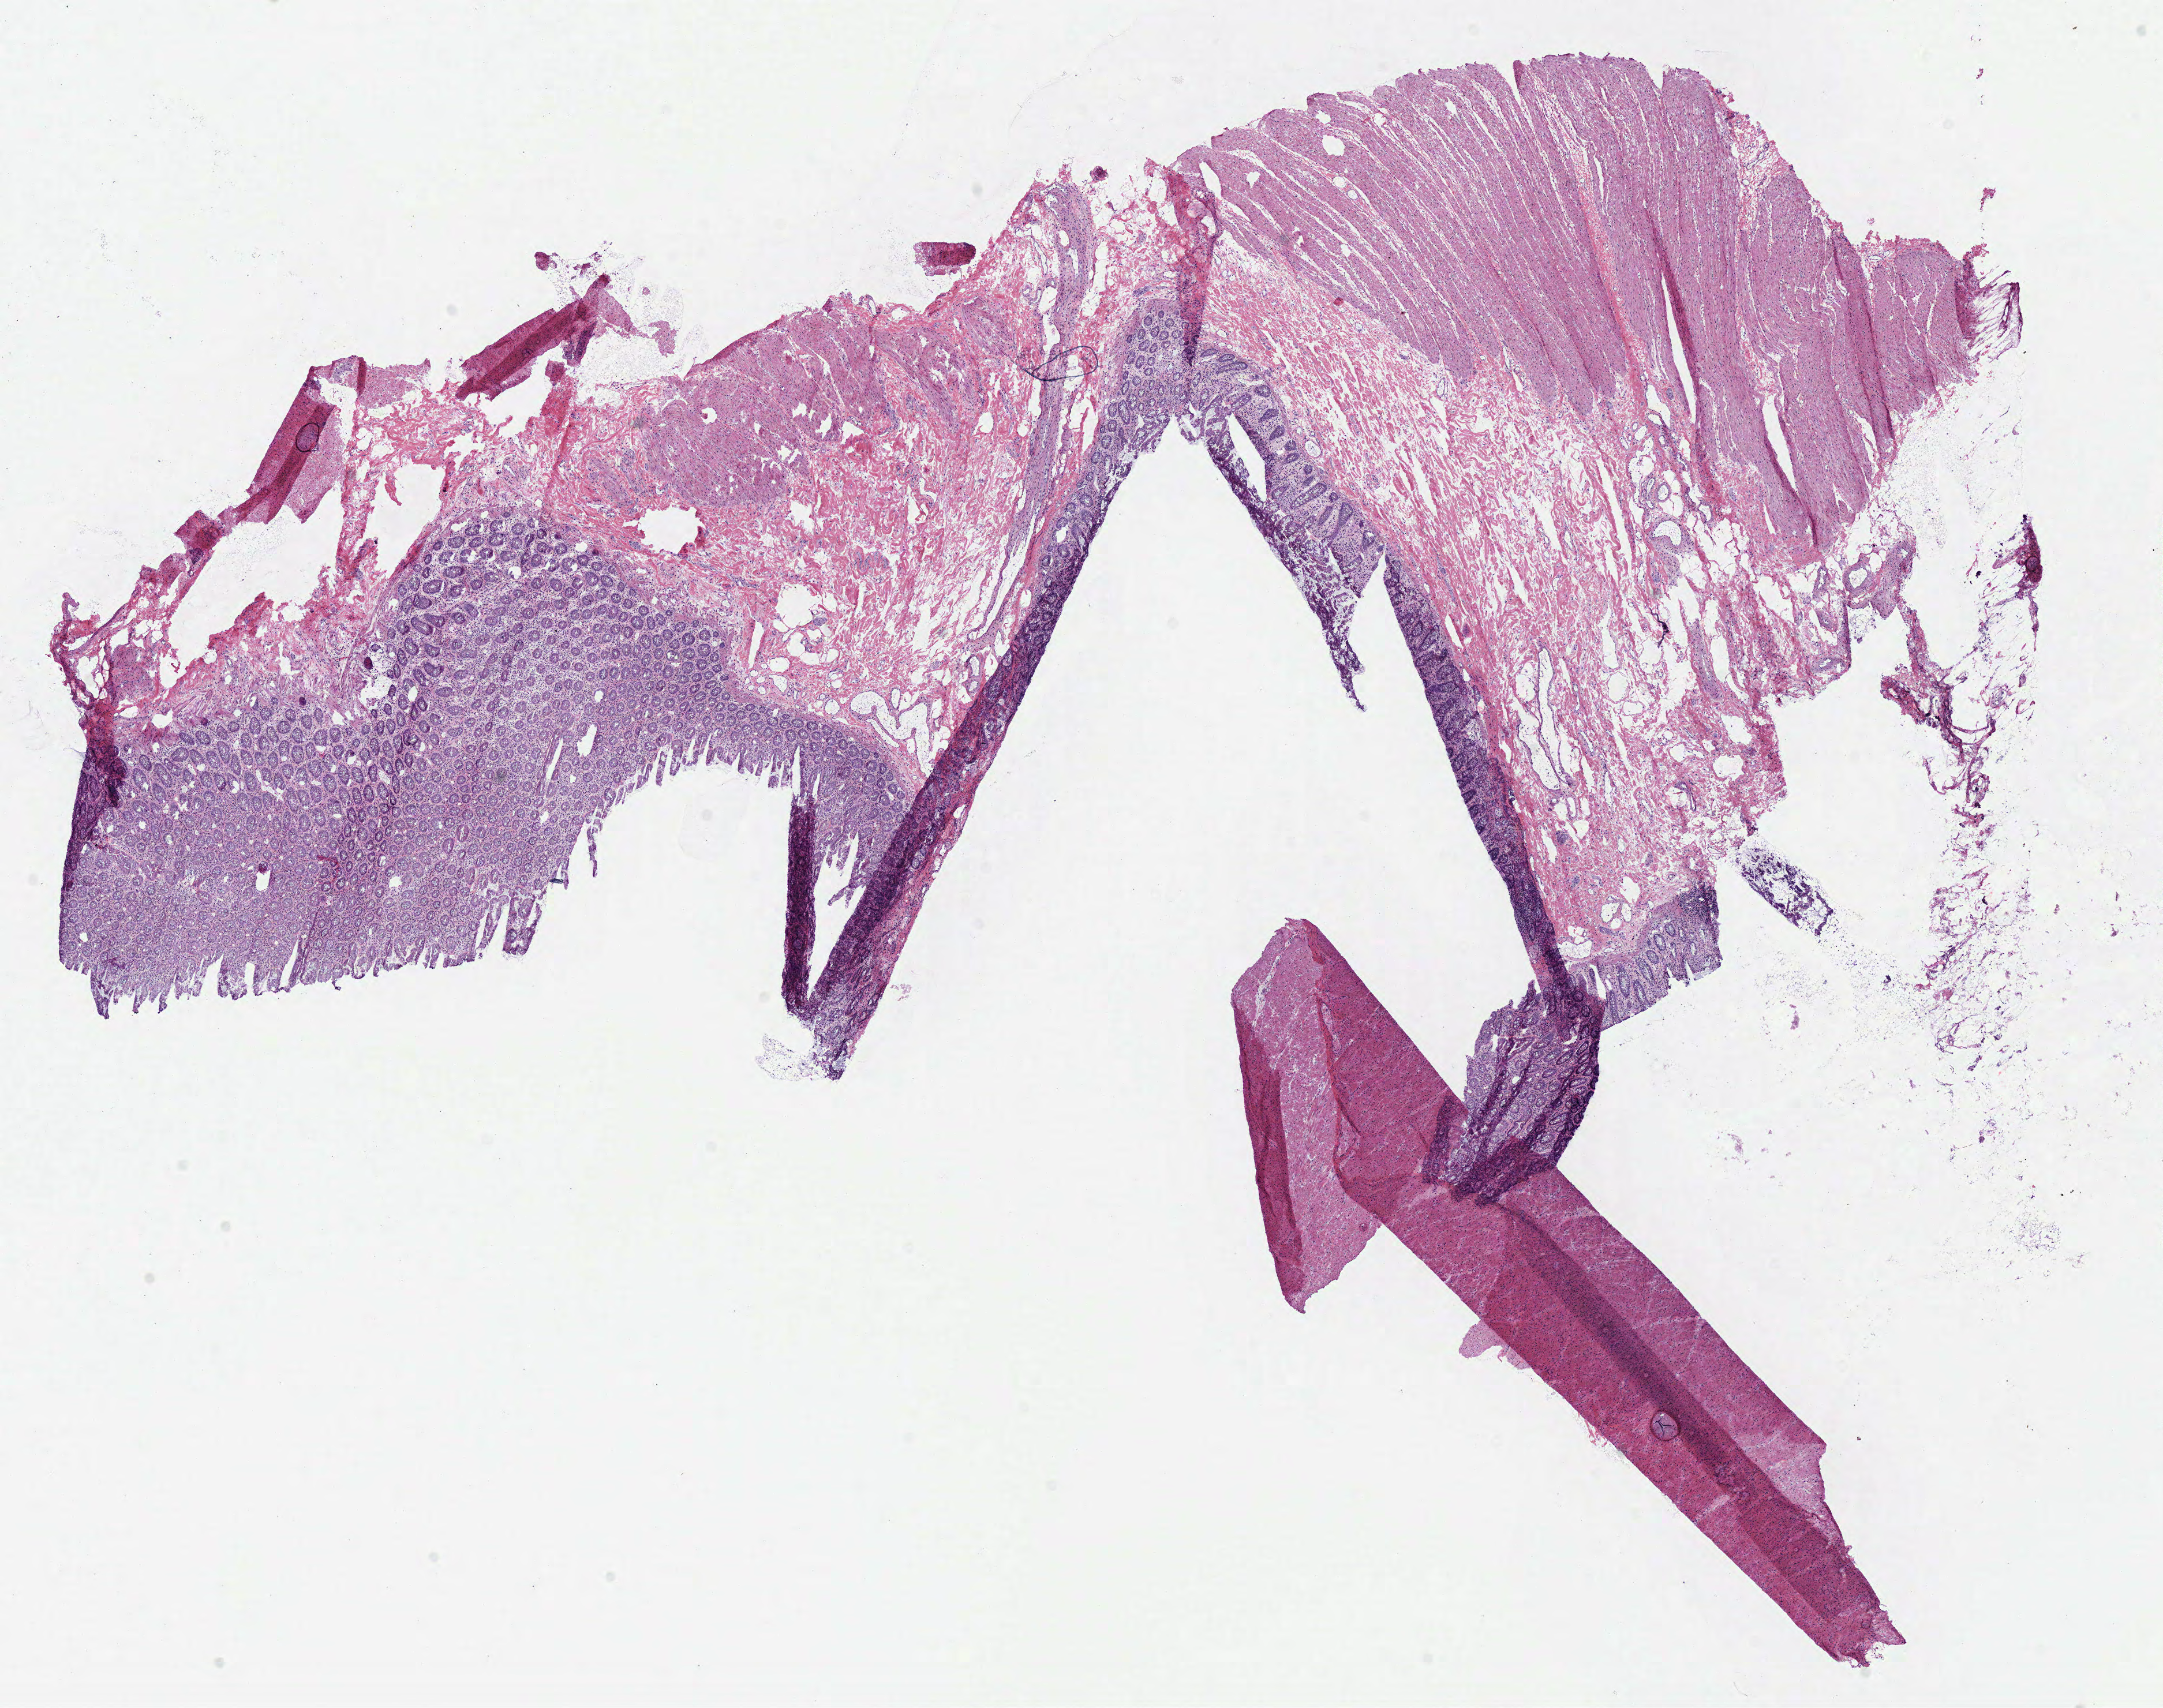
Digitized H&E tissue section (whole slide) — a low-resolution overview of the entire scanned area, about 14.8 x 11.7 mm (acquisition: 40x scan), frozen section from the top of the tissue portion, colon, solid tissue normal (non-tumour tissue) sample. Patient: male, age at initial diagnosis 60 years.
This section: solid tissue normal sample (biorepository sample class). Patient diagnosis: Mucinous adenocarcinoma (sigmoid colon).